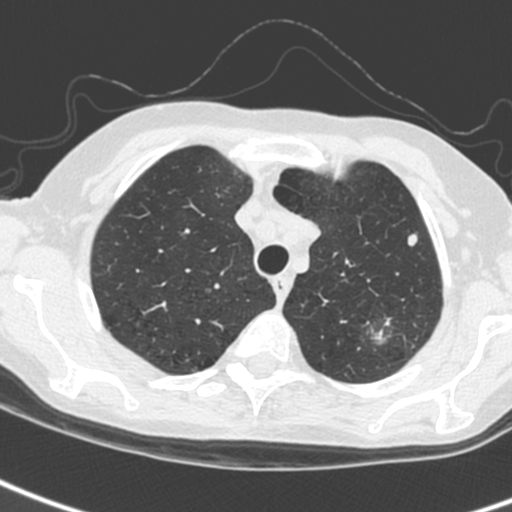
Low-dose screening chest CT, axial slice. Baseline annual screen. Lung window (W 1500 / L -600 HU). 1.3 mm slice thickness. Standard (soft-tissue) reconstruction kernel (C). Slice 34 of 242 in the series. 512 × 512 image matrix. Female, age 61 years at enrolment.
2 expert reader's lesion annotations on this slice (largest first), bounding box <355,308,413,353> (left, top, right, bottom; pixels); <395,225,431,257>. The screening reader recorded 2 non-calcified nodules or masses ≥4 mm on this exam (left upper lobe, left upper lobe); which of them these boxes mark is not recorded. Official screen result: positive, change unspecified: nodule(s) >= 4 mm or enlarging nodule(s), mass(es), or other non-specific abnormalities suspicious for lung cancer.